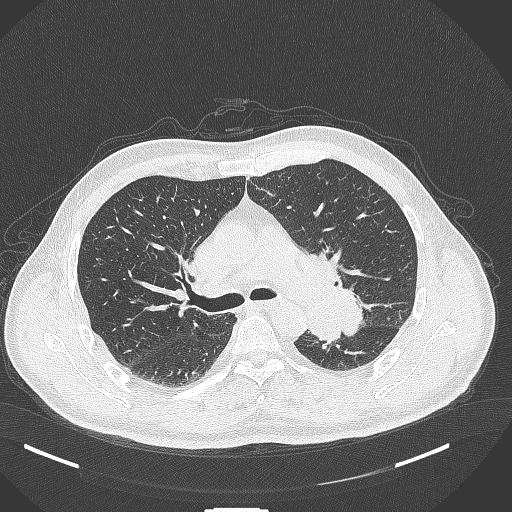
Chest CT, one axial slice; slice 264 of 429 in the series (ordered by position); reconstruction kernel B70f; lung window (W 1500 / L -600 HU); 1 mm slice thickness; 512 × 512 image matrix, field of view 400 × 400 mm. Patient: male, 55 years. Case-level facts recorded for this patient, not image findings: clinical TNM (as recorded): T3 N0 M1c; histopathological grade: G3.
Outlined on this slice (bounding box drawn by a radiologist):
- lung tumour (recorded histology: adenocarcinoma): bounding box <305,279,370,353> (left, top, right, bottom; pixels)